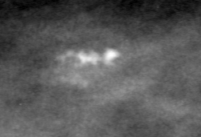
Cropped region of a digitized screen-film mammogram centred on a radiologist-marked abnormality; right breast; CC view; BI-RADS breast density category 3 (scale 1–4).
- Calcifications, morphology dystrophic, distribution clustered; BI-RADS assessment category 3; subtlety rating 4 on a 1 (subtle) to 5 (obvious) scale; pathology result (as recorded, not read from the image): benign.